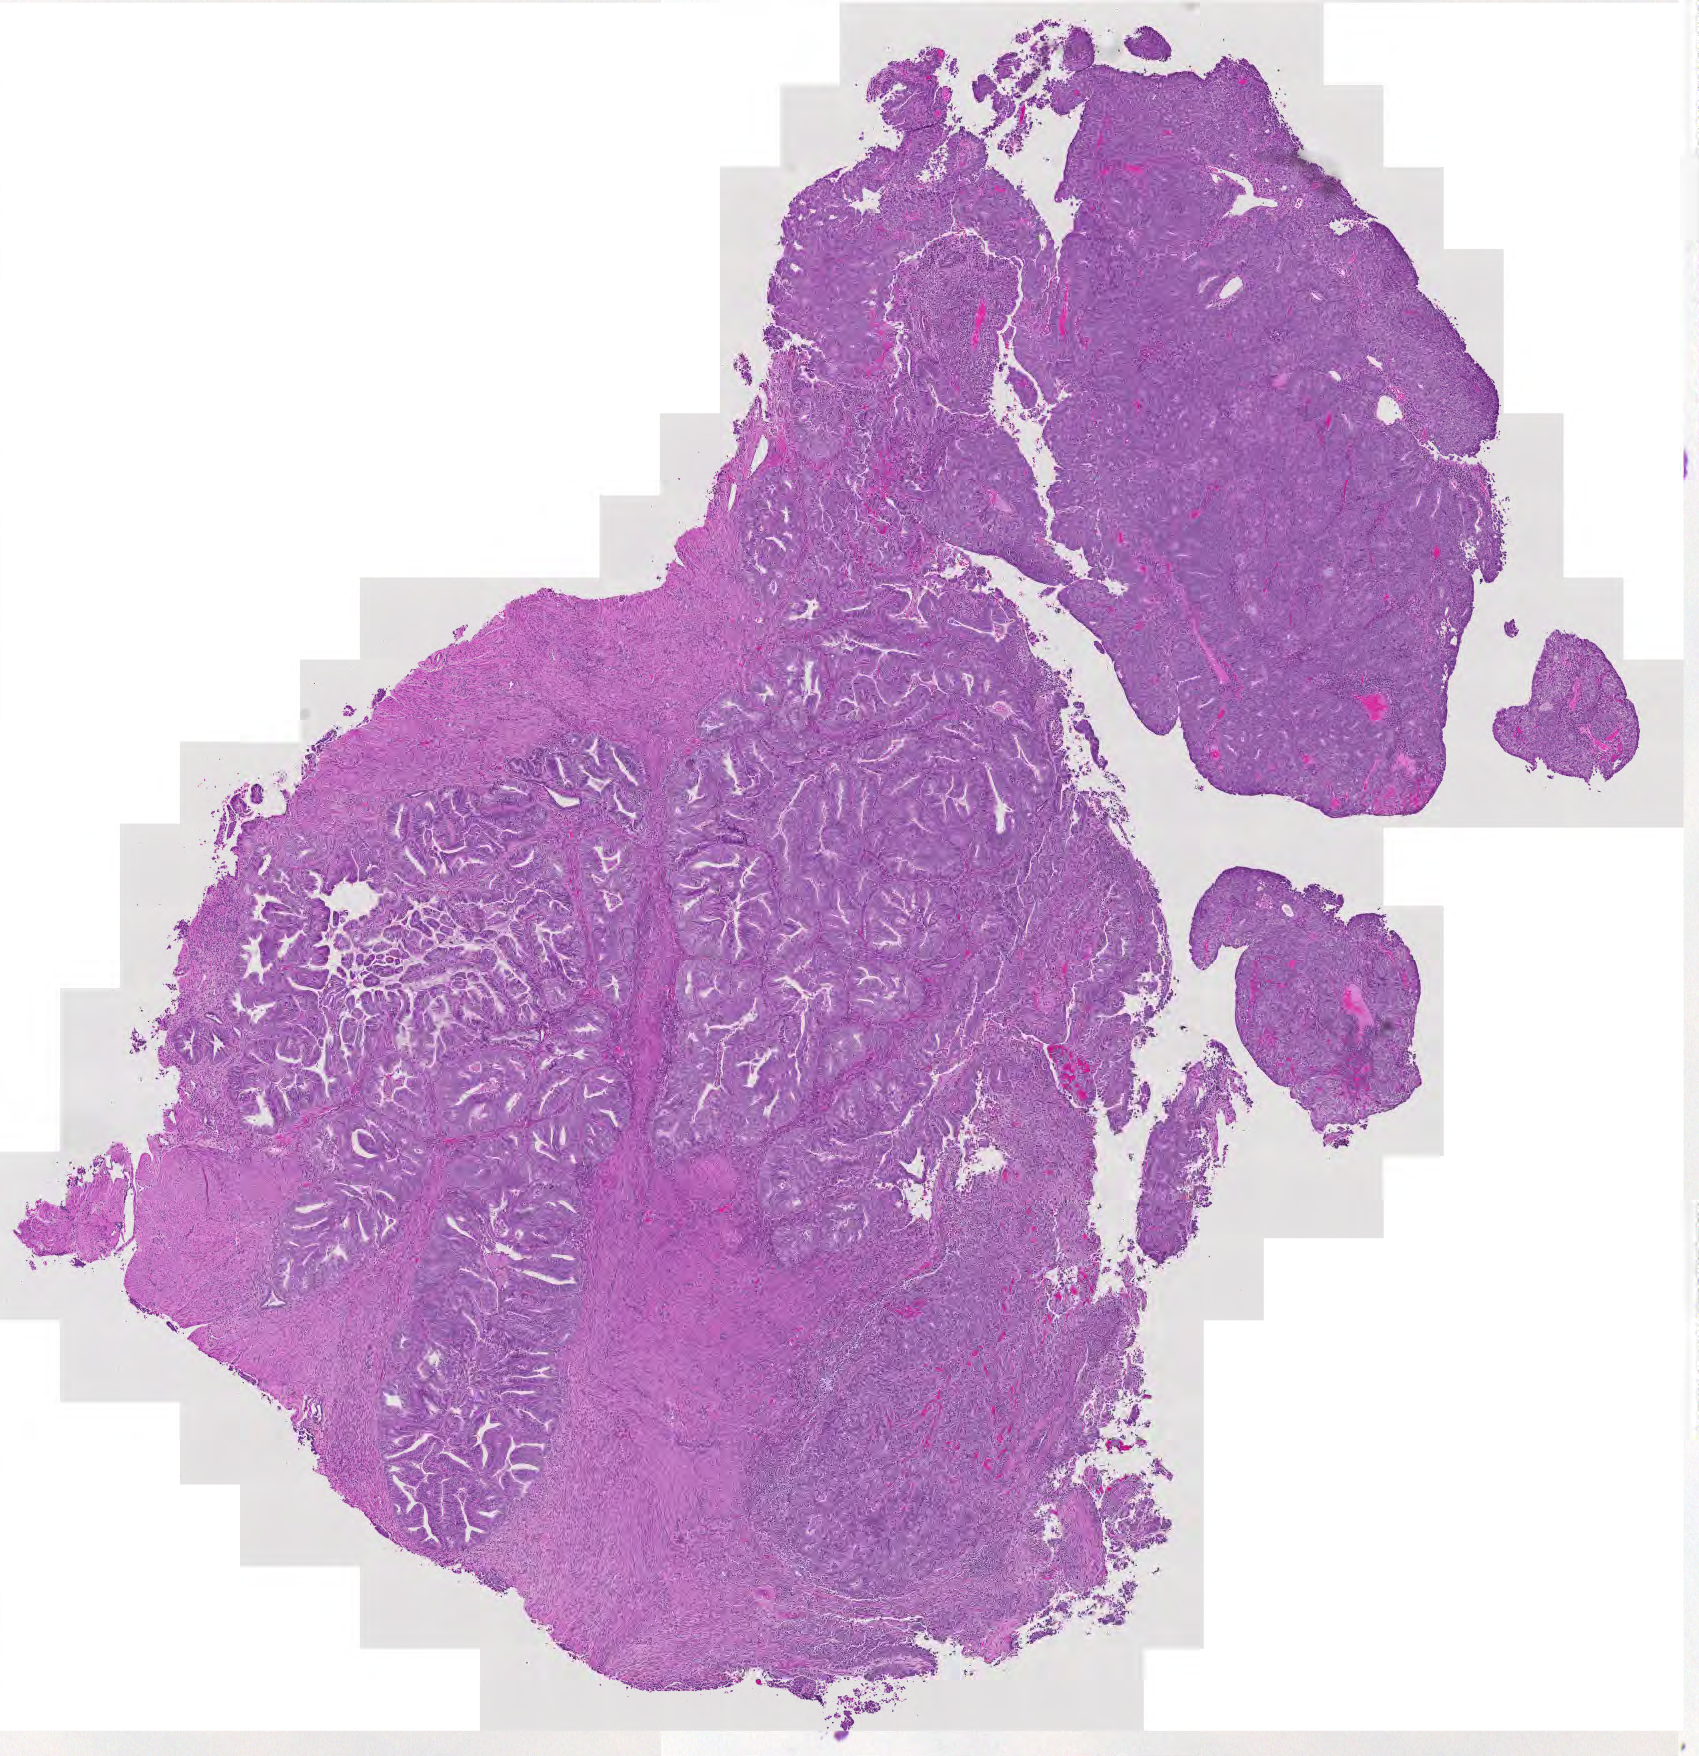
Hematoxylin and eosin (H&E) stained whole-slide image — low-resolution overview of the scanned area, about 8.8 x 9.1 mm. Tumour tissue sample, uterus. Female, 54 y/o. Histologic grade: G2 (moderately differentiated).
- histologic diagnosis: Endometrioid adenocarcinoma, NOS
- AJCC pathologic stage: I